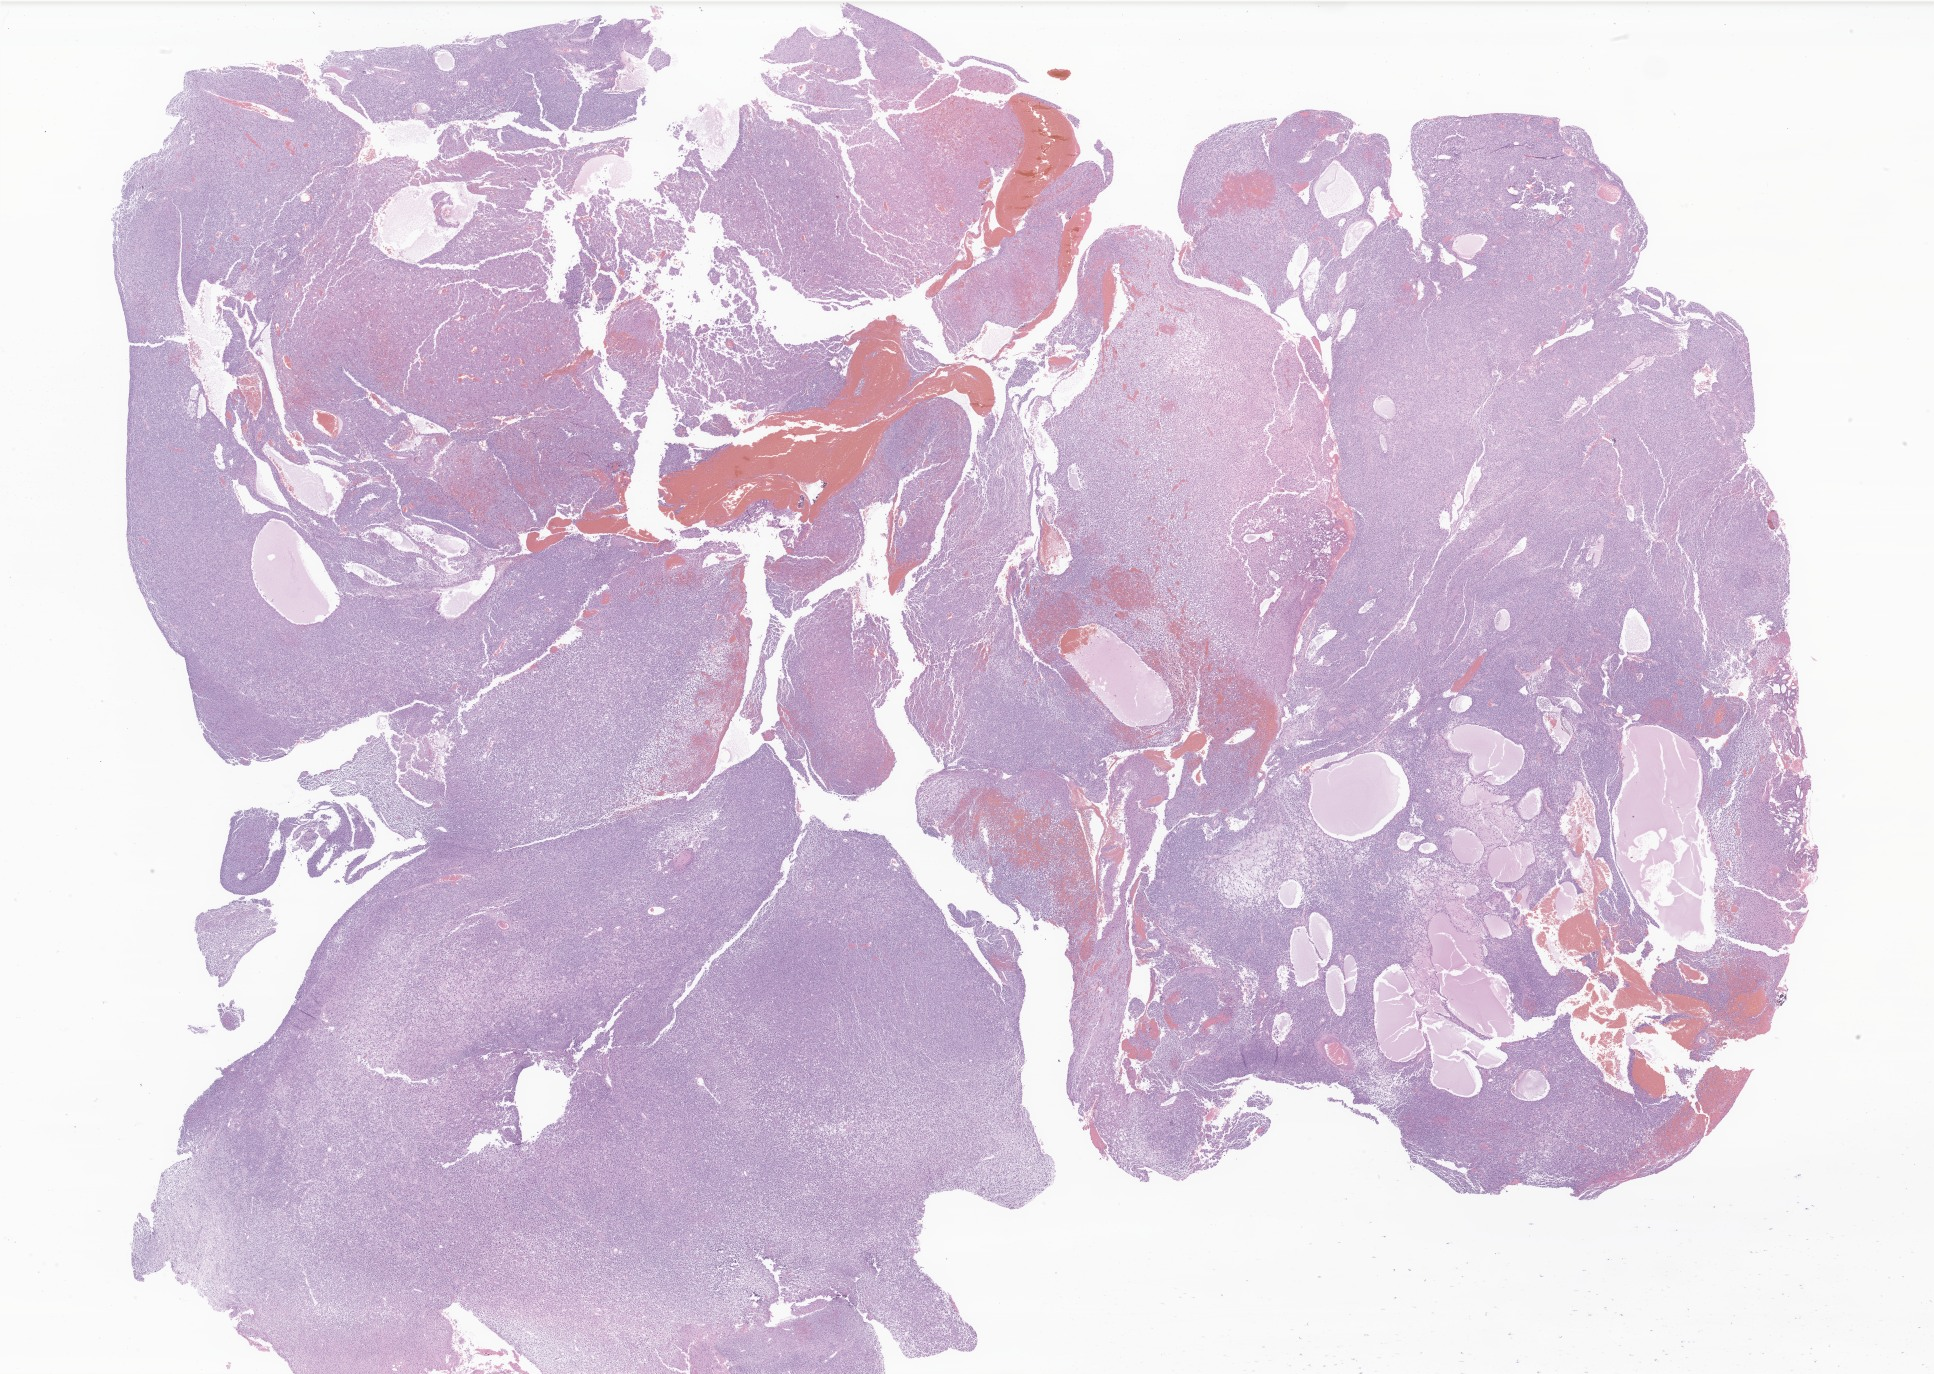
Hematoxylin and eosin (H&E) whole-slide image of tumor tissue from the pleura — whole scanned area (about 32.6 x 23.2 mm) shown as a low-resolution overview. FFPE section. Patient: male, age 57 months (4 years 9 months).
Recorded diagnosis: Pleuropulmonary blastoma.